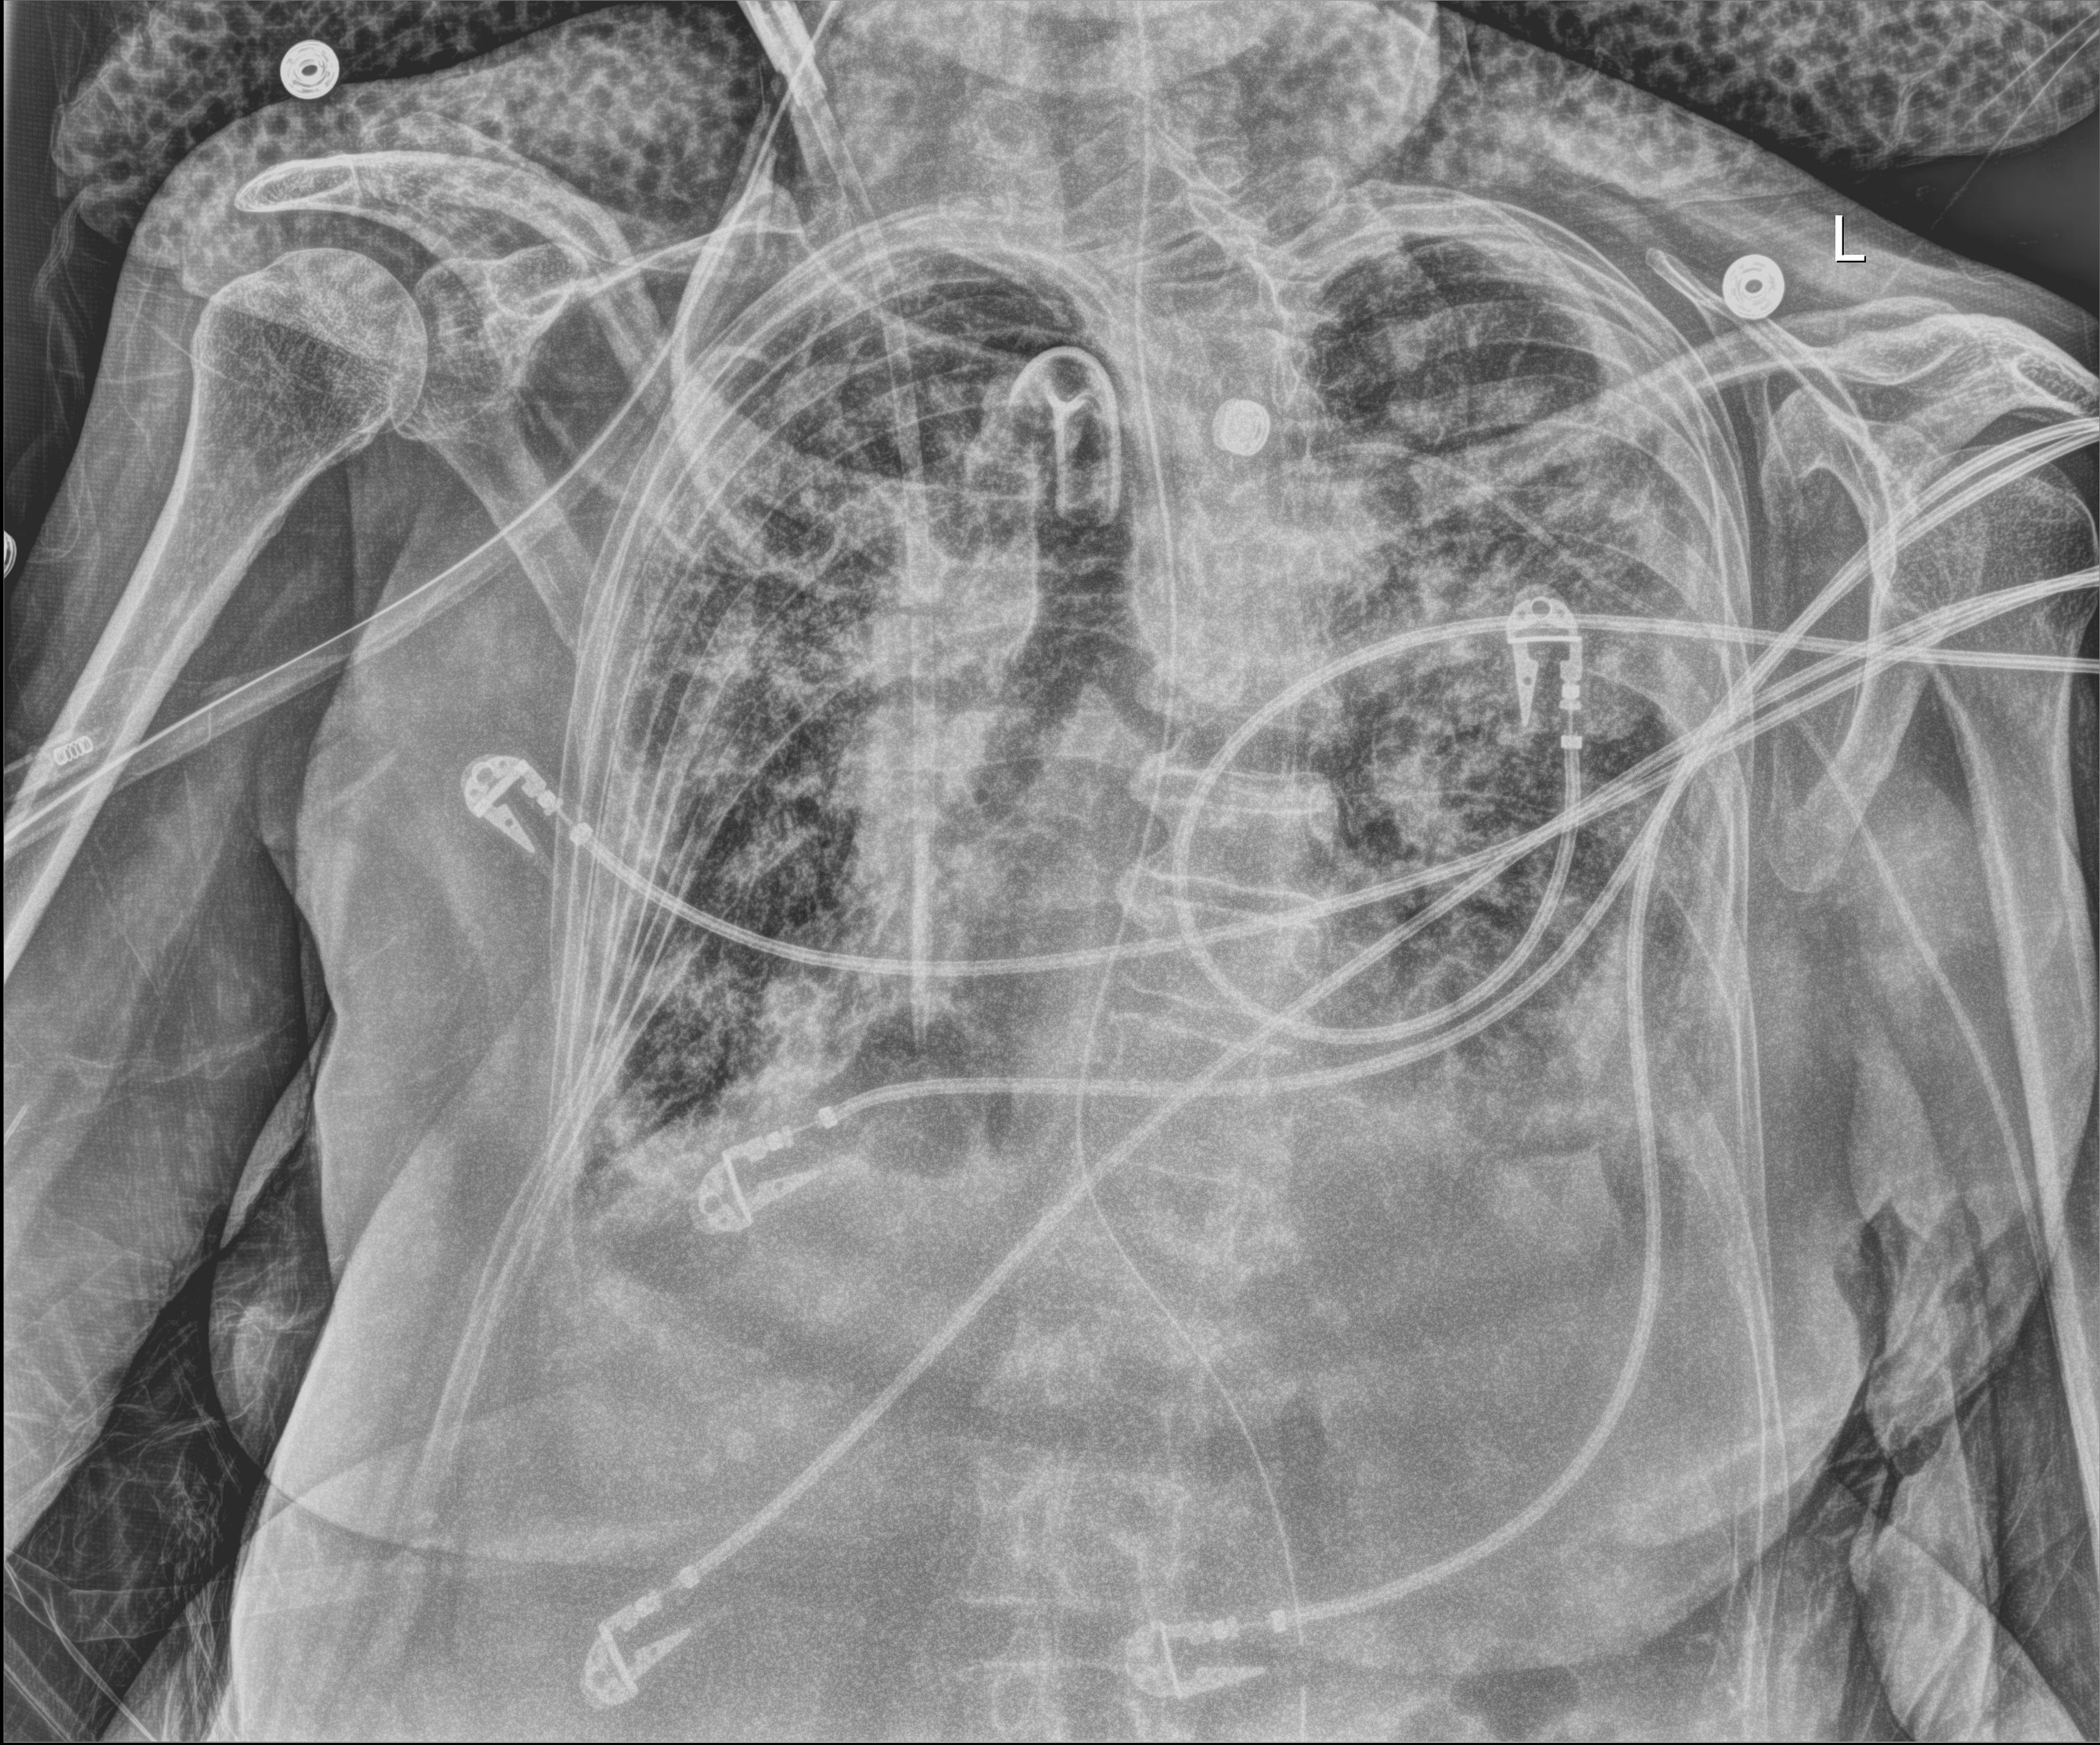
Portable chest radiograph, anteroposterior (AP) projection. Female patient hospitalised with COVID-19, age 75–90 years.
Admission-level facts for this patient (not findings on this image; timing relative to this image not recorded): mechanically ventilated during this hospital stay: yes.